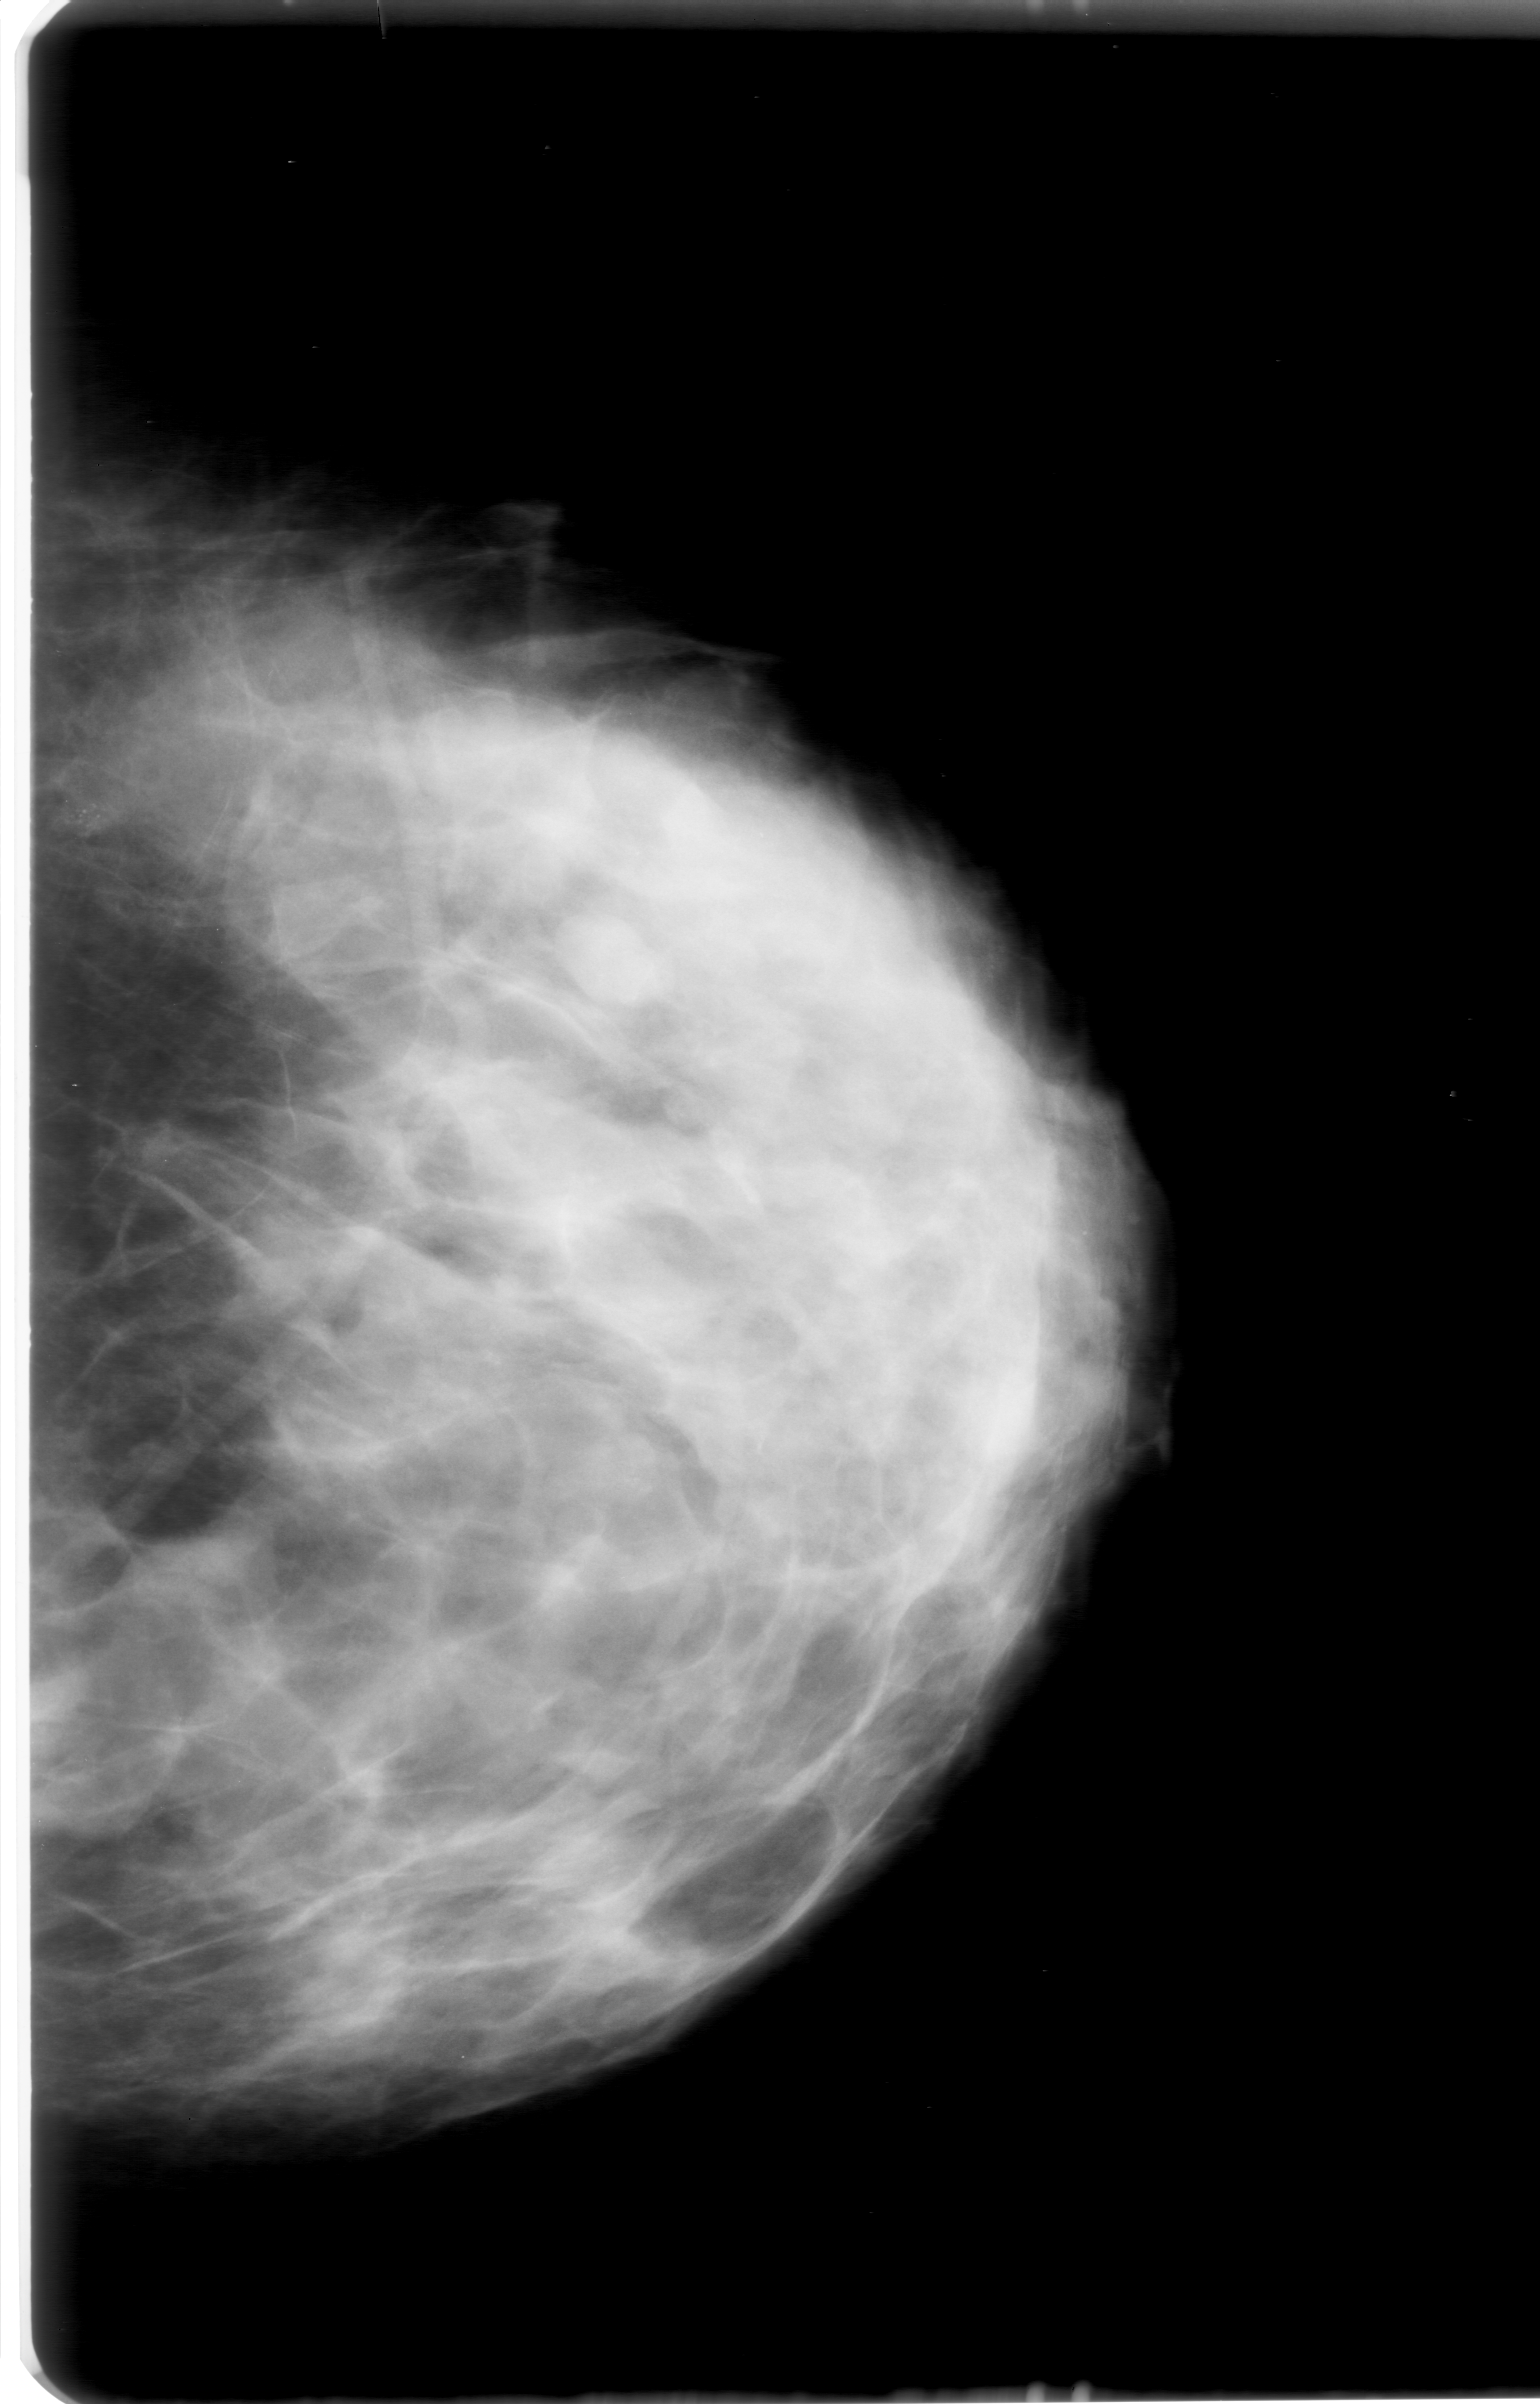
Scanned film-screen mammogram. Left breast. CC view. Breast composition: heterogeneously dense (BI-RADS density category 3 of 4). 1540 × 2404 image matrix.
Expert-marked regions of interest on this film, with their recorded descriptors:
- calcifications, morphology round and regular / pleomorphic, distribution clustered; BI-RADS assessment category 0; pathology (as recorded): benign: bounding box <38,748,179,889> (left, top, right, bottom; pixels)